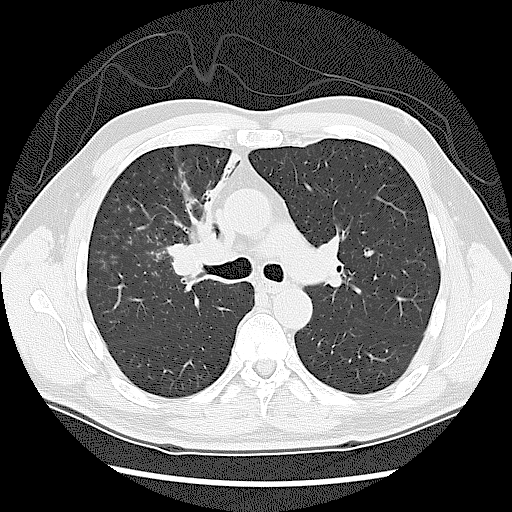
Chest CT (low-dose screening protocol), one axial image, first (baseline) screen, lung window (W 1500 / L -600 HU), 120 kVp, slice 51 of 131 in the series, 512 × 512 image matrix. Male participant, aged 60 years at enrolment. Current smoker at enrolment.
Lesion marked by an expert reader, bounding box (x1, y1, x2, y2) in pixels: (158, 221, 242, 315). Screening reader's record for this exam: no non-calcified nodule ≥4 mm recorded. Participant outcome: lung cancer diagnosed 41 days after this screen — small cell carcinoma, NOS, right upper lobe, stage IIIA (AJCC 6th edition).